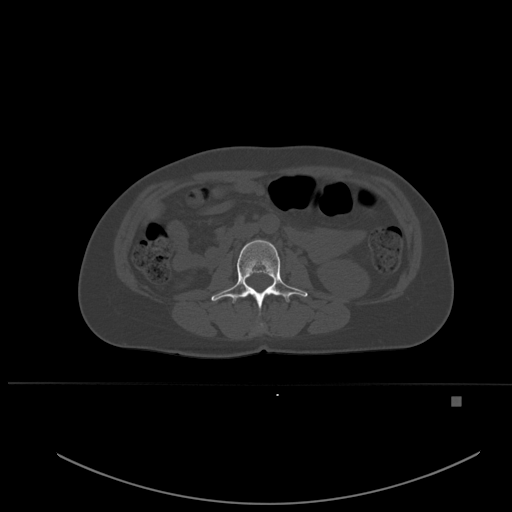
CT including the spine, one axial slice. Position 214 of 651 along the scan axis. Bone window (W 1800 / L 400 HU). 512 × 512 image matrix, field of view 443 × 443 mm. Patient: female, 49 years. Case-level facts recorded for this patient, not image findings: primary cancer: breast.
Outlined on this slice (semi-automatically segmented with operator editing):
- L1 vertebra: bounding box (x1, y1, x2, y2) in pixels: (260, 323, 263, 326)
- L2 vertebra: (211, 239, 308, 309)